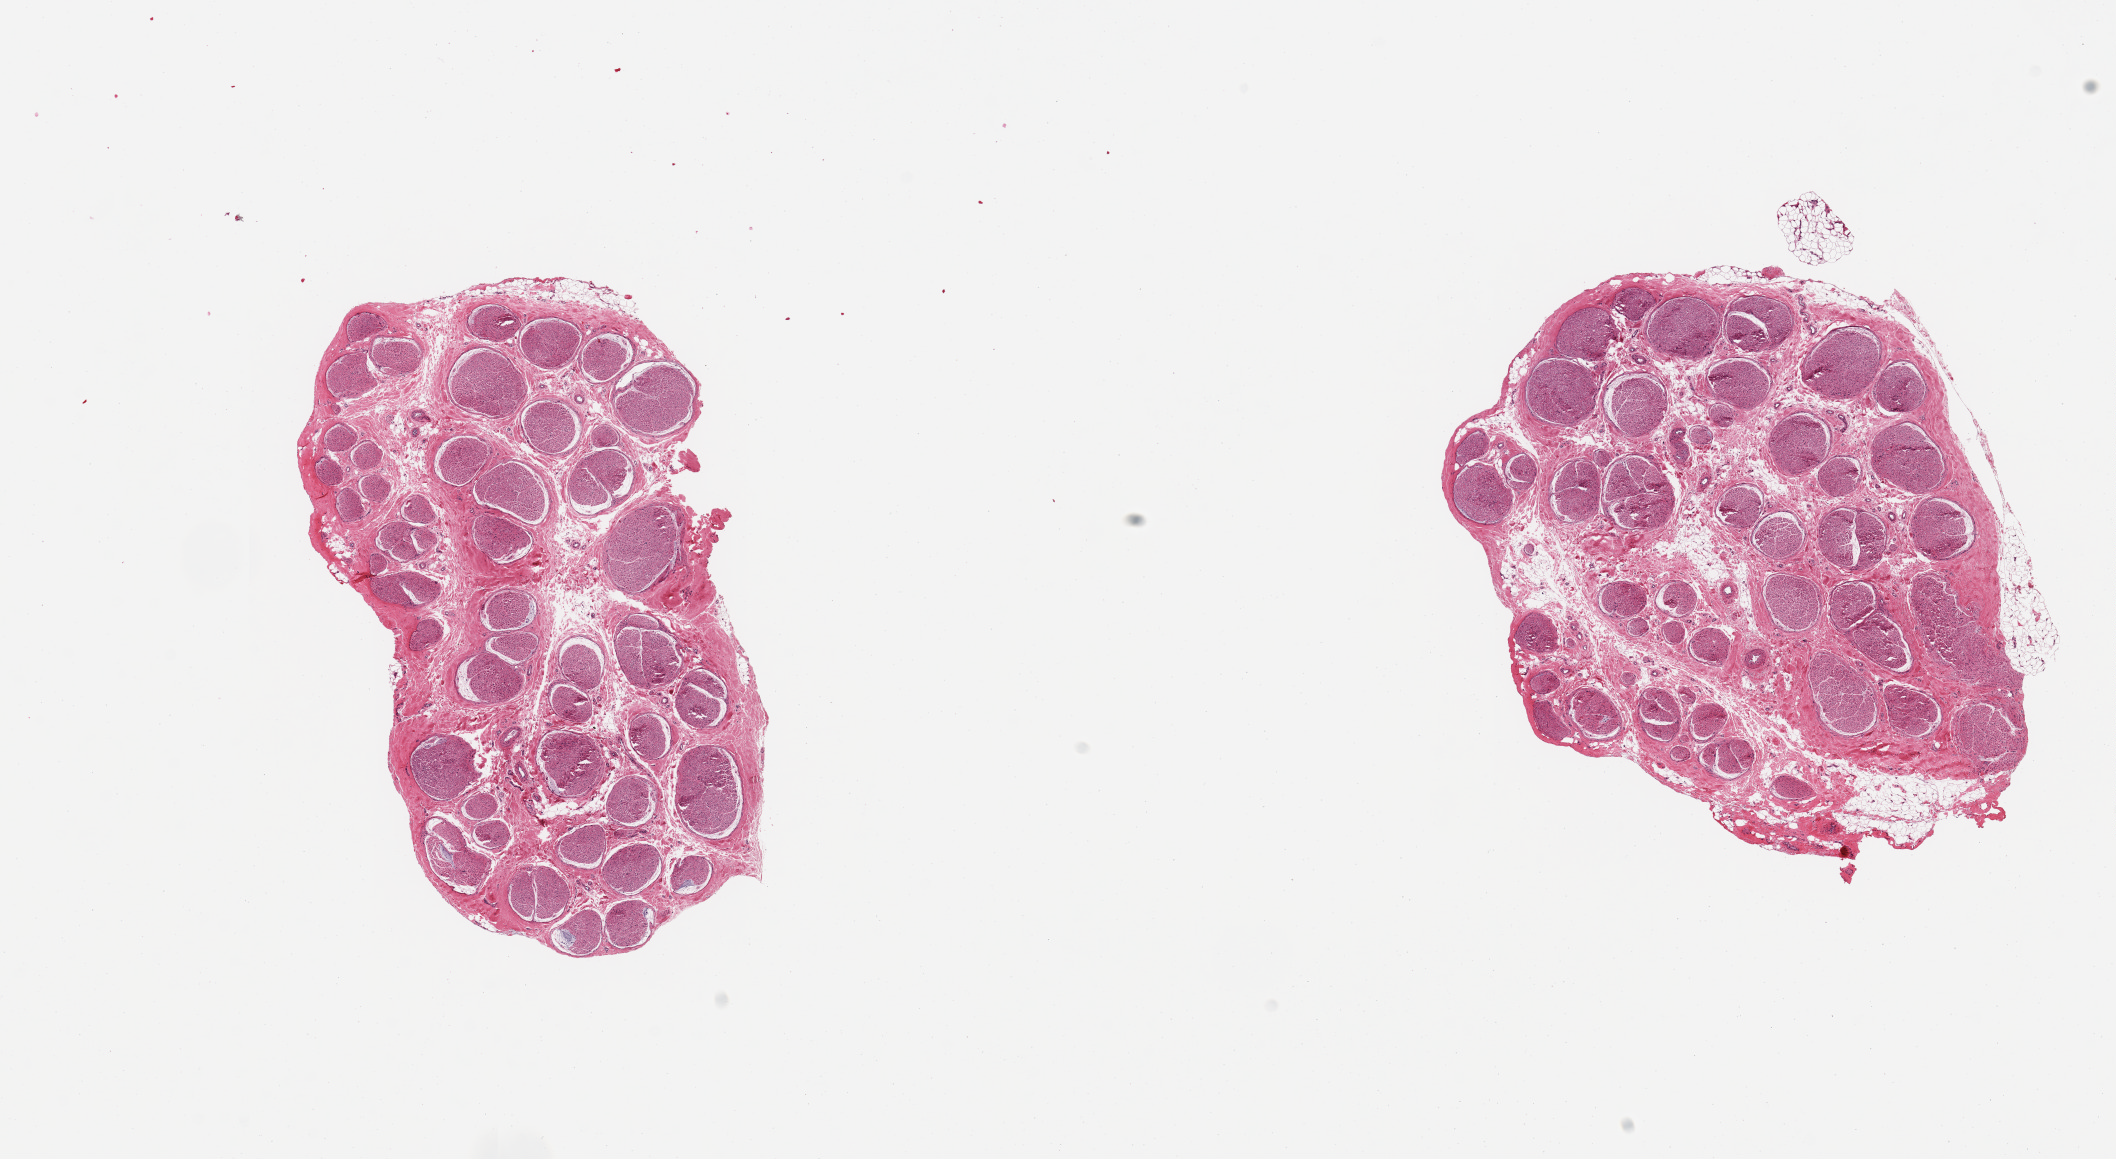
Haematoxylin and eosin whole-slide image — low-resolution overview of the scanned area, about 16.7 x 9.2 mm, PAXgene-fixed paraffin-embedded (PFPE) section, target tissue: tibial nerve, donor tissue sample. Female donor.
Pathologist's review note for this sample: 2 pieces; relatively well trimmed.